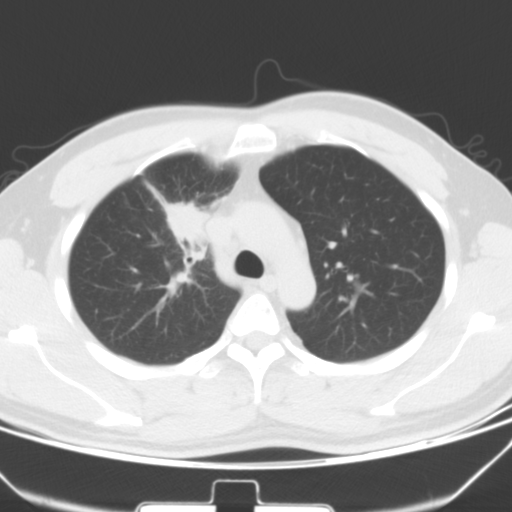
Chest CT, one axial slice; position 43 of 60 along the scan axis; 120 kVp; lung window (W 1500 / L -600 HU); 5 mm slice thickness; 512 × 512 image matrix. Male patient, age 35 years. From the clinical record (not read from this slice): clinical TNM (as recorded): T1c N1 M1b.
Annotated regions visible in this slice (bounding box drawn by a radiologist):
- lung tumour (recorded histology: adenocarcinoma): bounding box (x1, y1, x2, y2) in pixels: (158, 192, 210, 255)